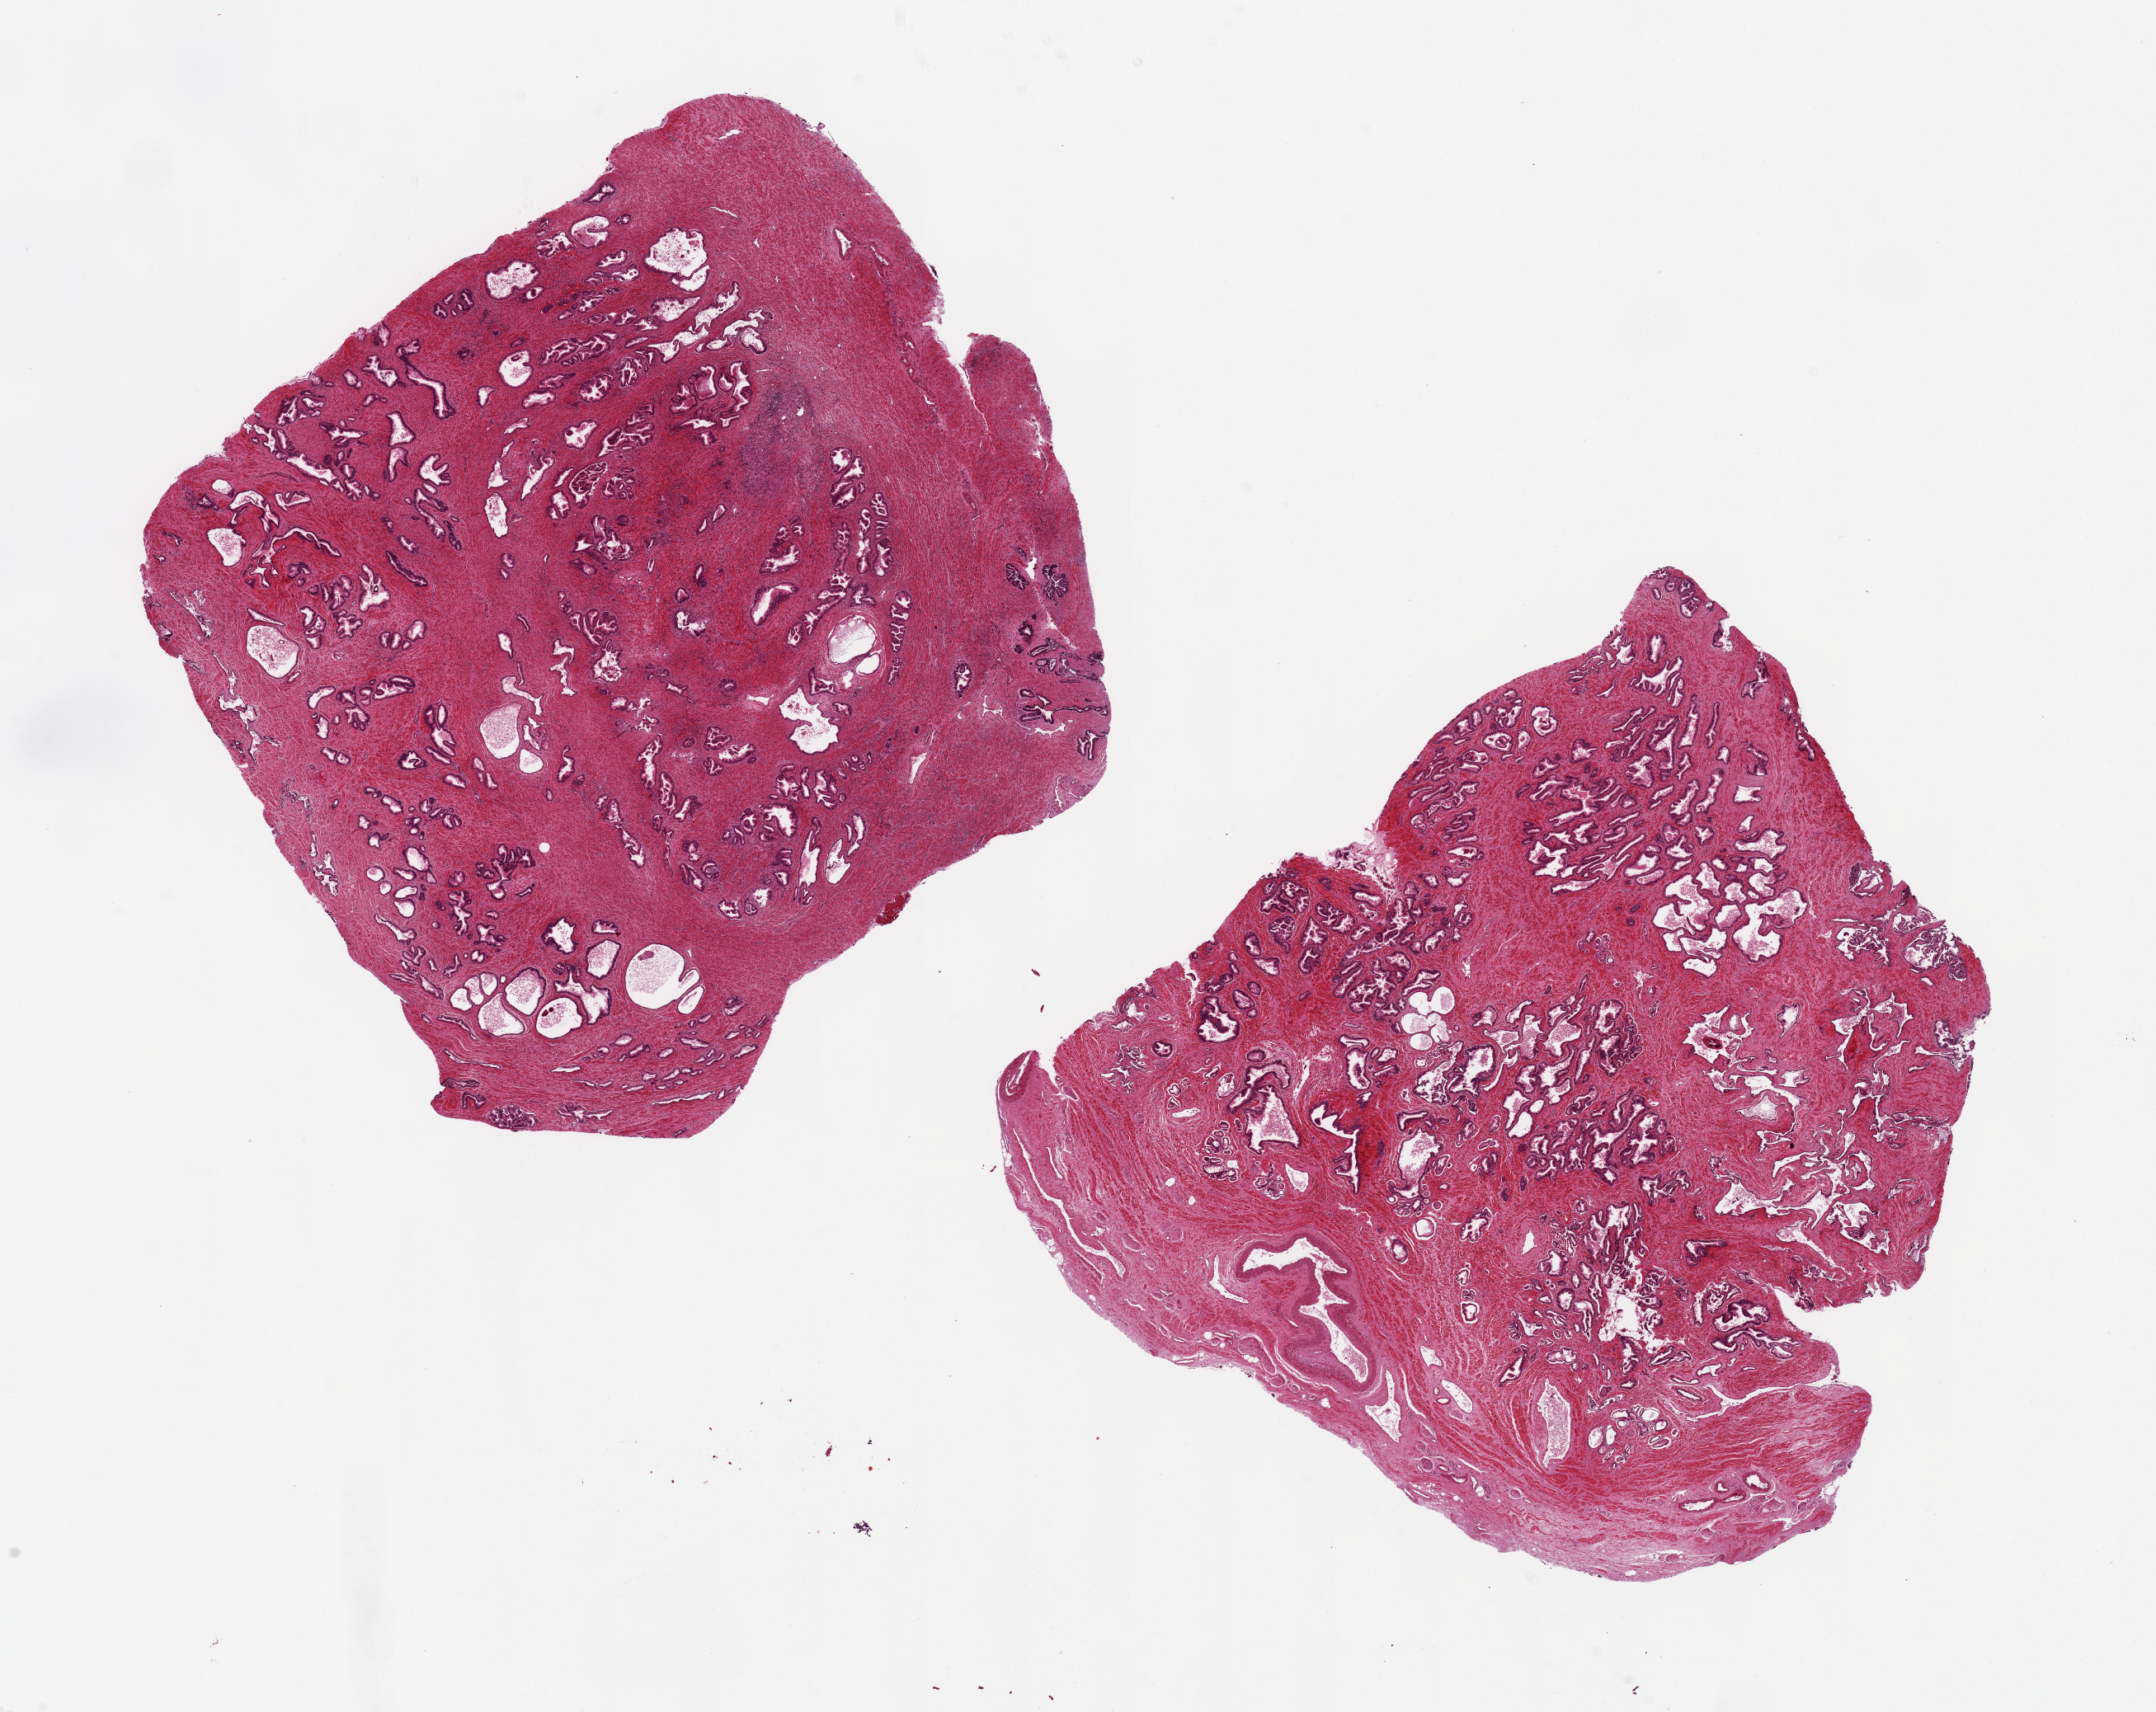
Whole-slide image, haematoxylin and eosin stain, a low-resolution overview of the entire scanned area, about 20.7 x 16.4 mm (acquisition: 20x scan), PAXgene-fixed, paraffin-embedded tissue, sampled site (target tissue): prostate, donor tissue sample. Male donor.
* reviewer comment on this tissue sample: 2 pieces, ~8x8 mm; mild atrophy